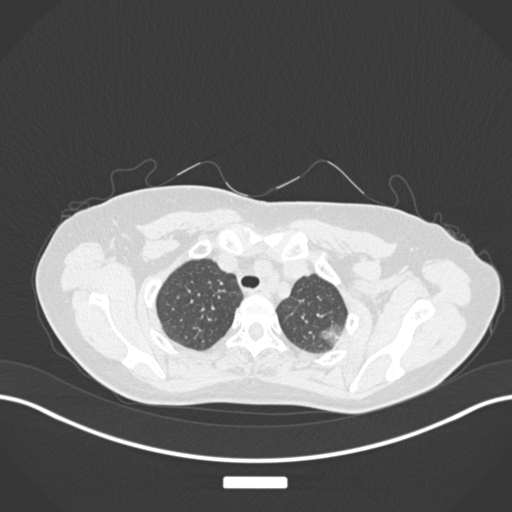
Chest CT, one axial slice; slice 147 of 181 in the series (ordered by position); reconstruction kernel B30f; lung window (W 1500 / L -600 HU); 1 mm slice thickness; 512 × 512 image matrix, field of view 400 × 400 mm. Female patient, age 58 years. From the clinical record (not read from this slice): clinical TNM (as recorded): T1c N0 M0.
Outlined on this slice (bounding box drawn by a radiologist):
- lung tumour (recorded histology: adenocarcinoma): bounding box [x1, y1, x2, y2] px = [319, 318, 345, 346]